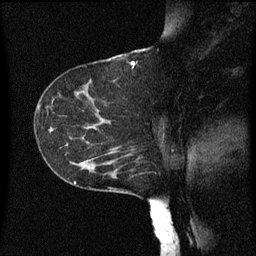
Breast MRI (dynamic contrast-enhanced), one sagittal slice. Slice 38 of 60 in the series (ordered by position). Dynamic contrast-enhanced series, image 2 of 3 at this slice position (ordered by acquisition). 1.5 T. TE 4.2 ms, TR 8 ms. 256 × 256 image matrix, field of view 200 × 200 mm. Patient: female, 55 years.
Outlined on this slice (semi-automatically segmented with operator editing):
- analysis volume of interest (the breast-tissue region the enhancement analysis was run in; not a lesion): bounding box (x1, y1, x2, y2) in pixels: (46, 124, 149, 179)
- tumour enhancement mask (voxels above the 70 % enhancement threshold inside the analysis volume of interest): (82, 142, 131, 171)